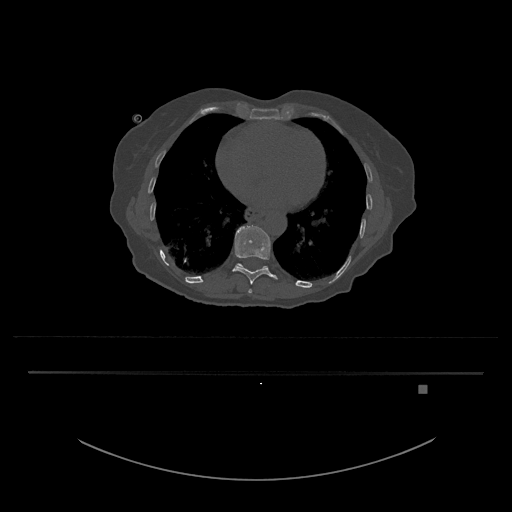
CT including the spine, one axial slice; bone window (W 1800 / L 400 HU); 0.5 mm slice thickness; 512 × 512 image matrix, field of view 500 × 500 mm. Female patient, age 57 years. Case-level facts recorded for this patient, not image findings: primary cancer: cervical.
Outlined on this slice (semi-automatic segmentation, software-assisted and operator-edited):
- T10 vertebra: box from (x=232, y=225) to (x=278, y=285) px
- T11 vertebra: (x=237, y=263)–(x=268, y=269)
- T9 vertebra: (x=248, y=289)–(x=252, y=293)